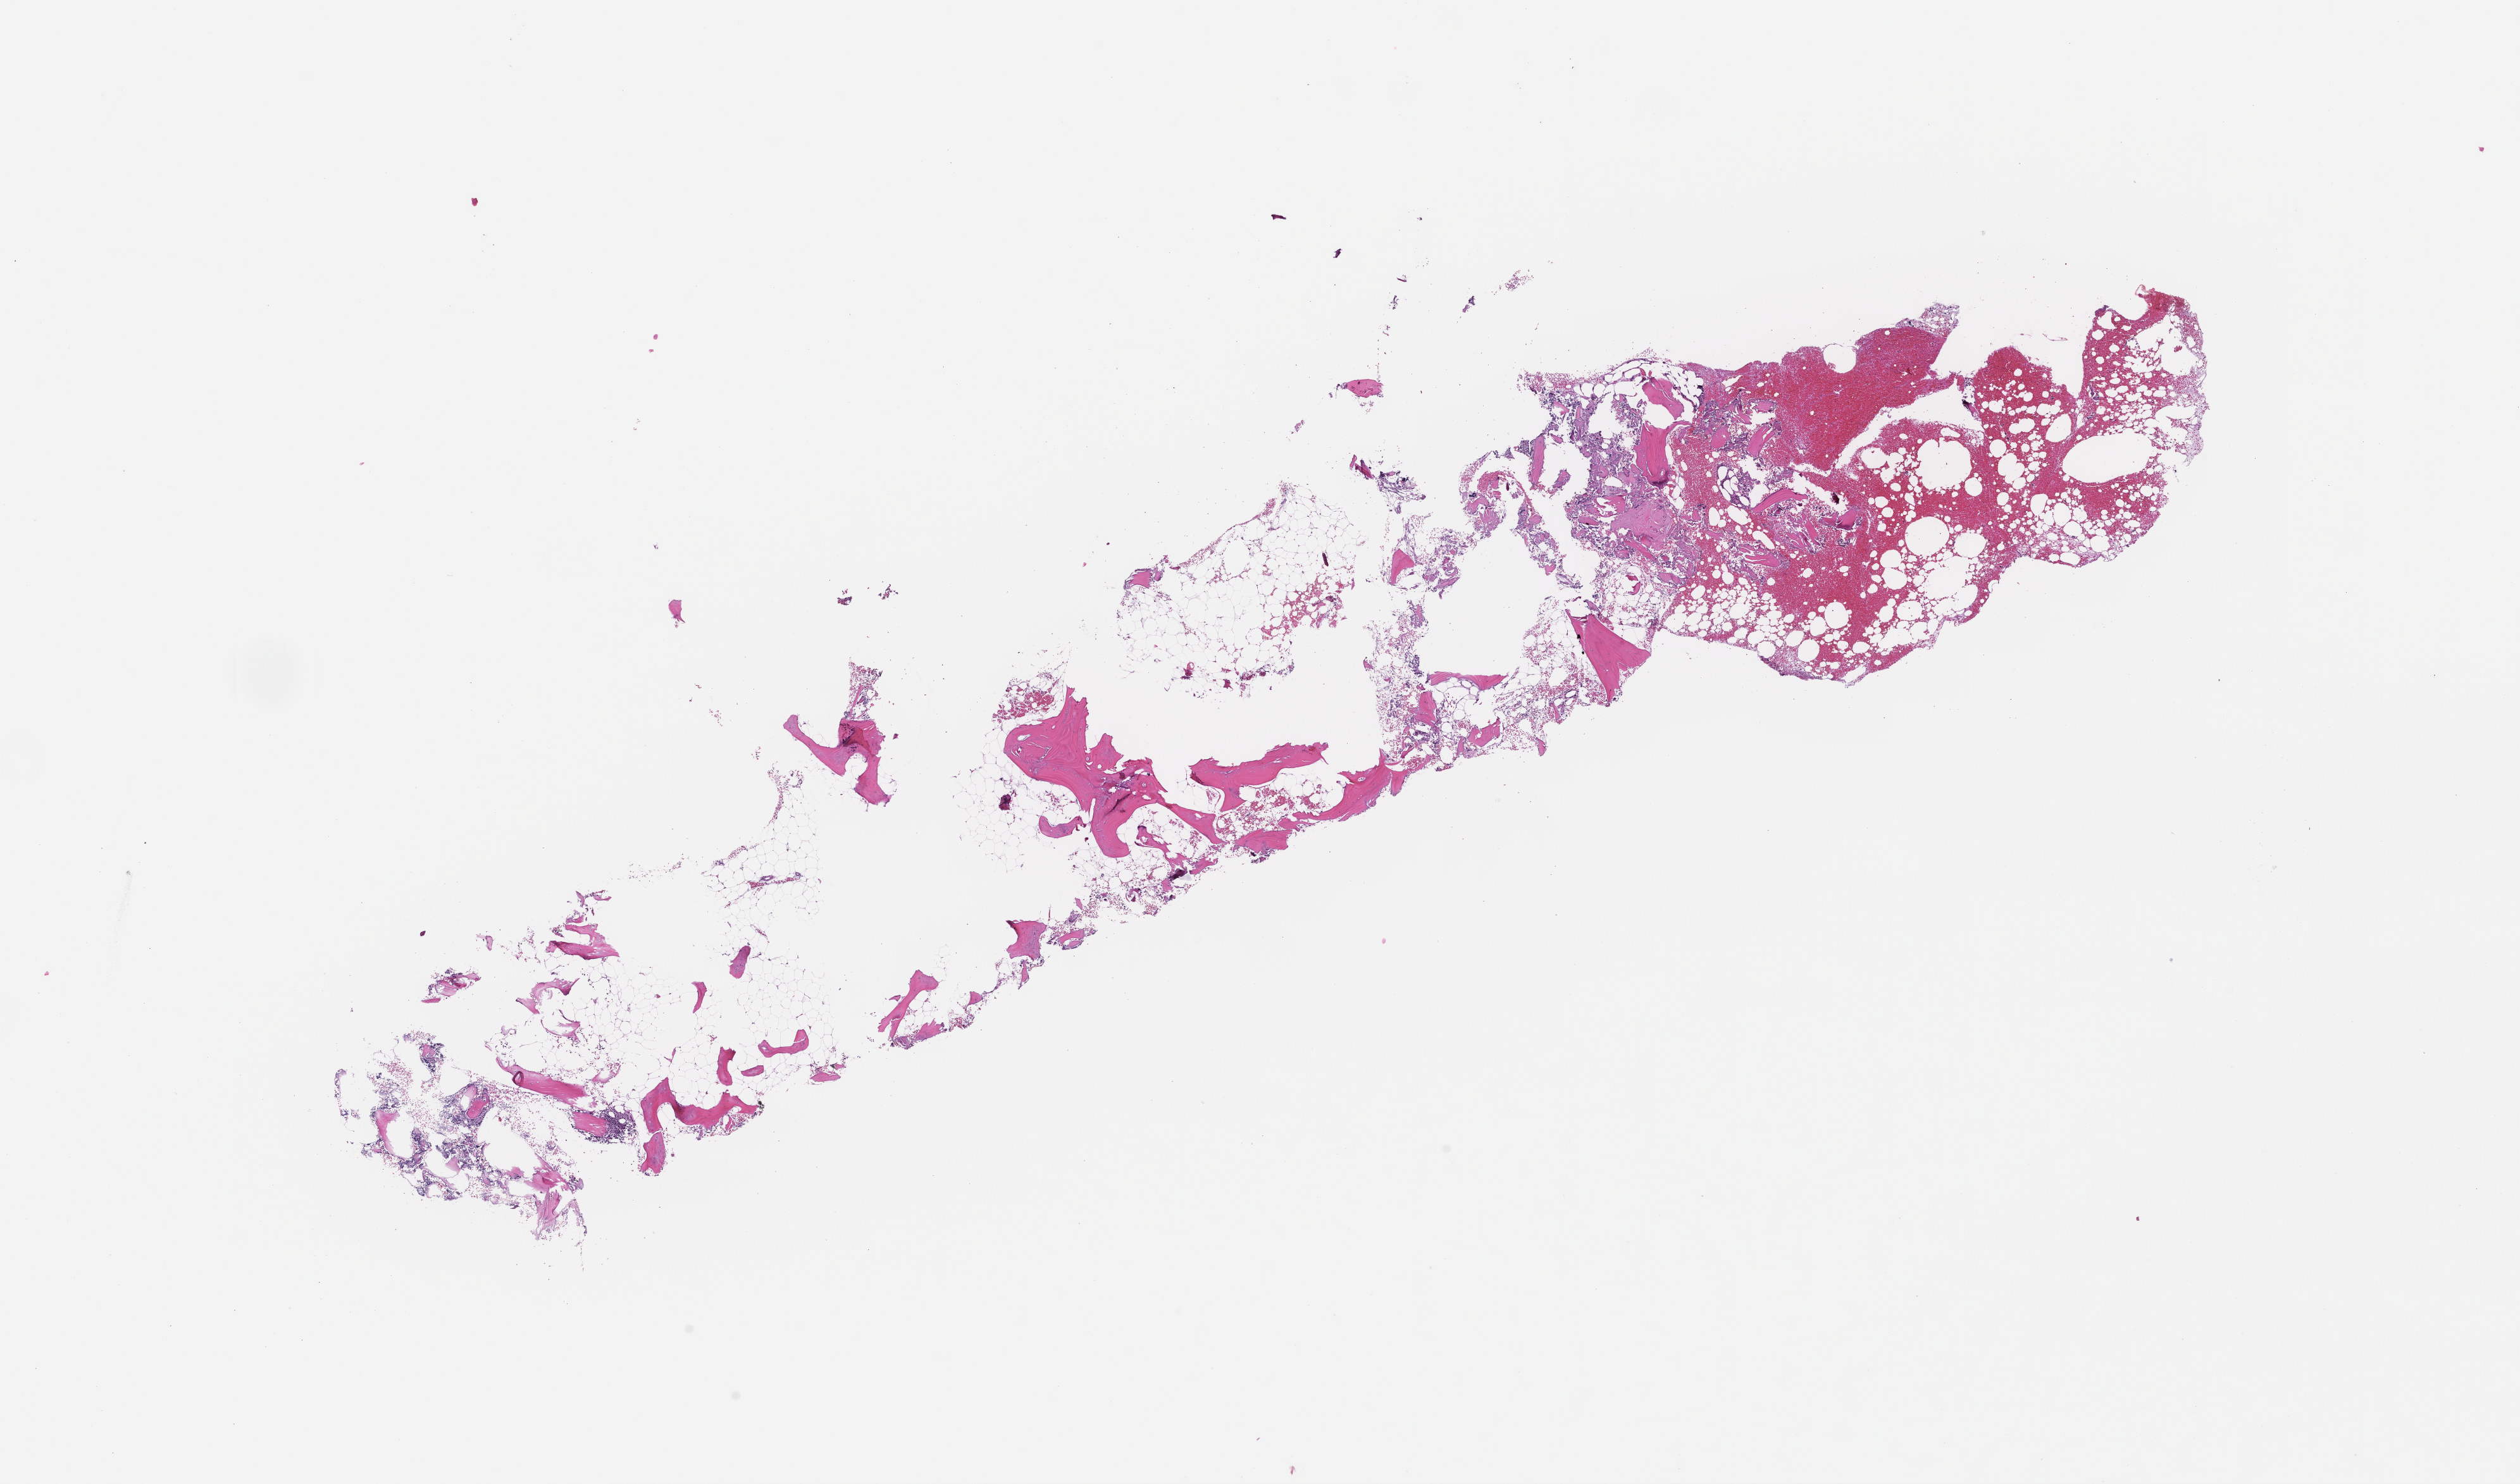
Digitized haematoxylin and eosin-stained section — whole scanned area (about 16.1 x 9.5 mm) shown as a low-resolution overview; formalin-fixed paraffin-embedded section; tissue site: bone marrow; specimen time point: collected on treatment. Patient: male.
• this section: primary tumour tissue
• diagnosis: Plasma Cell Myeloma